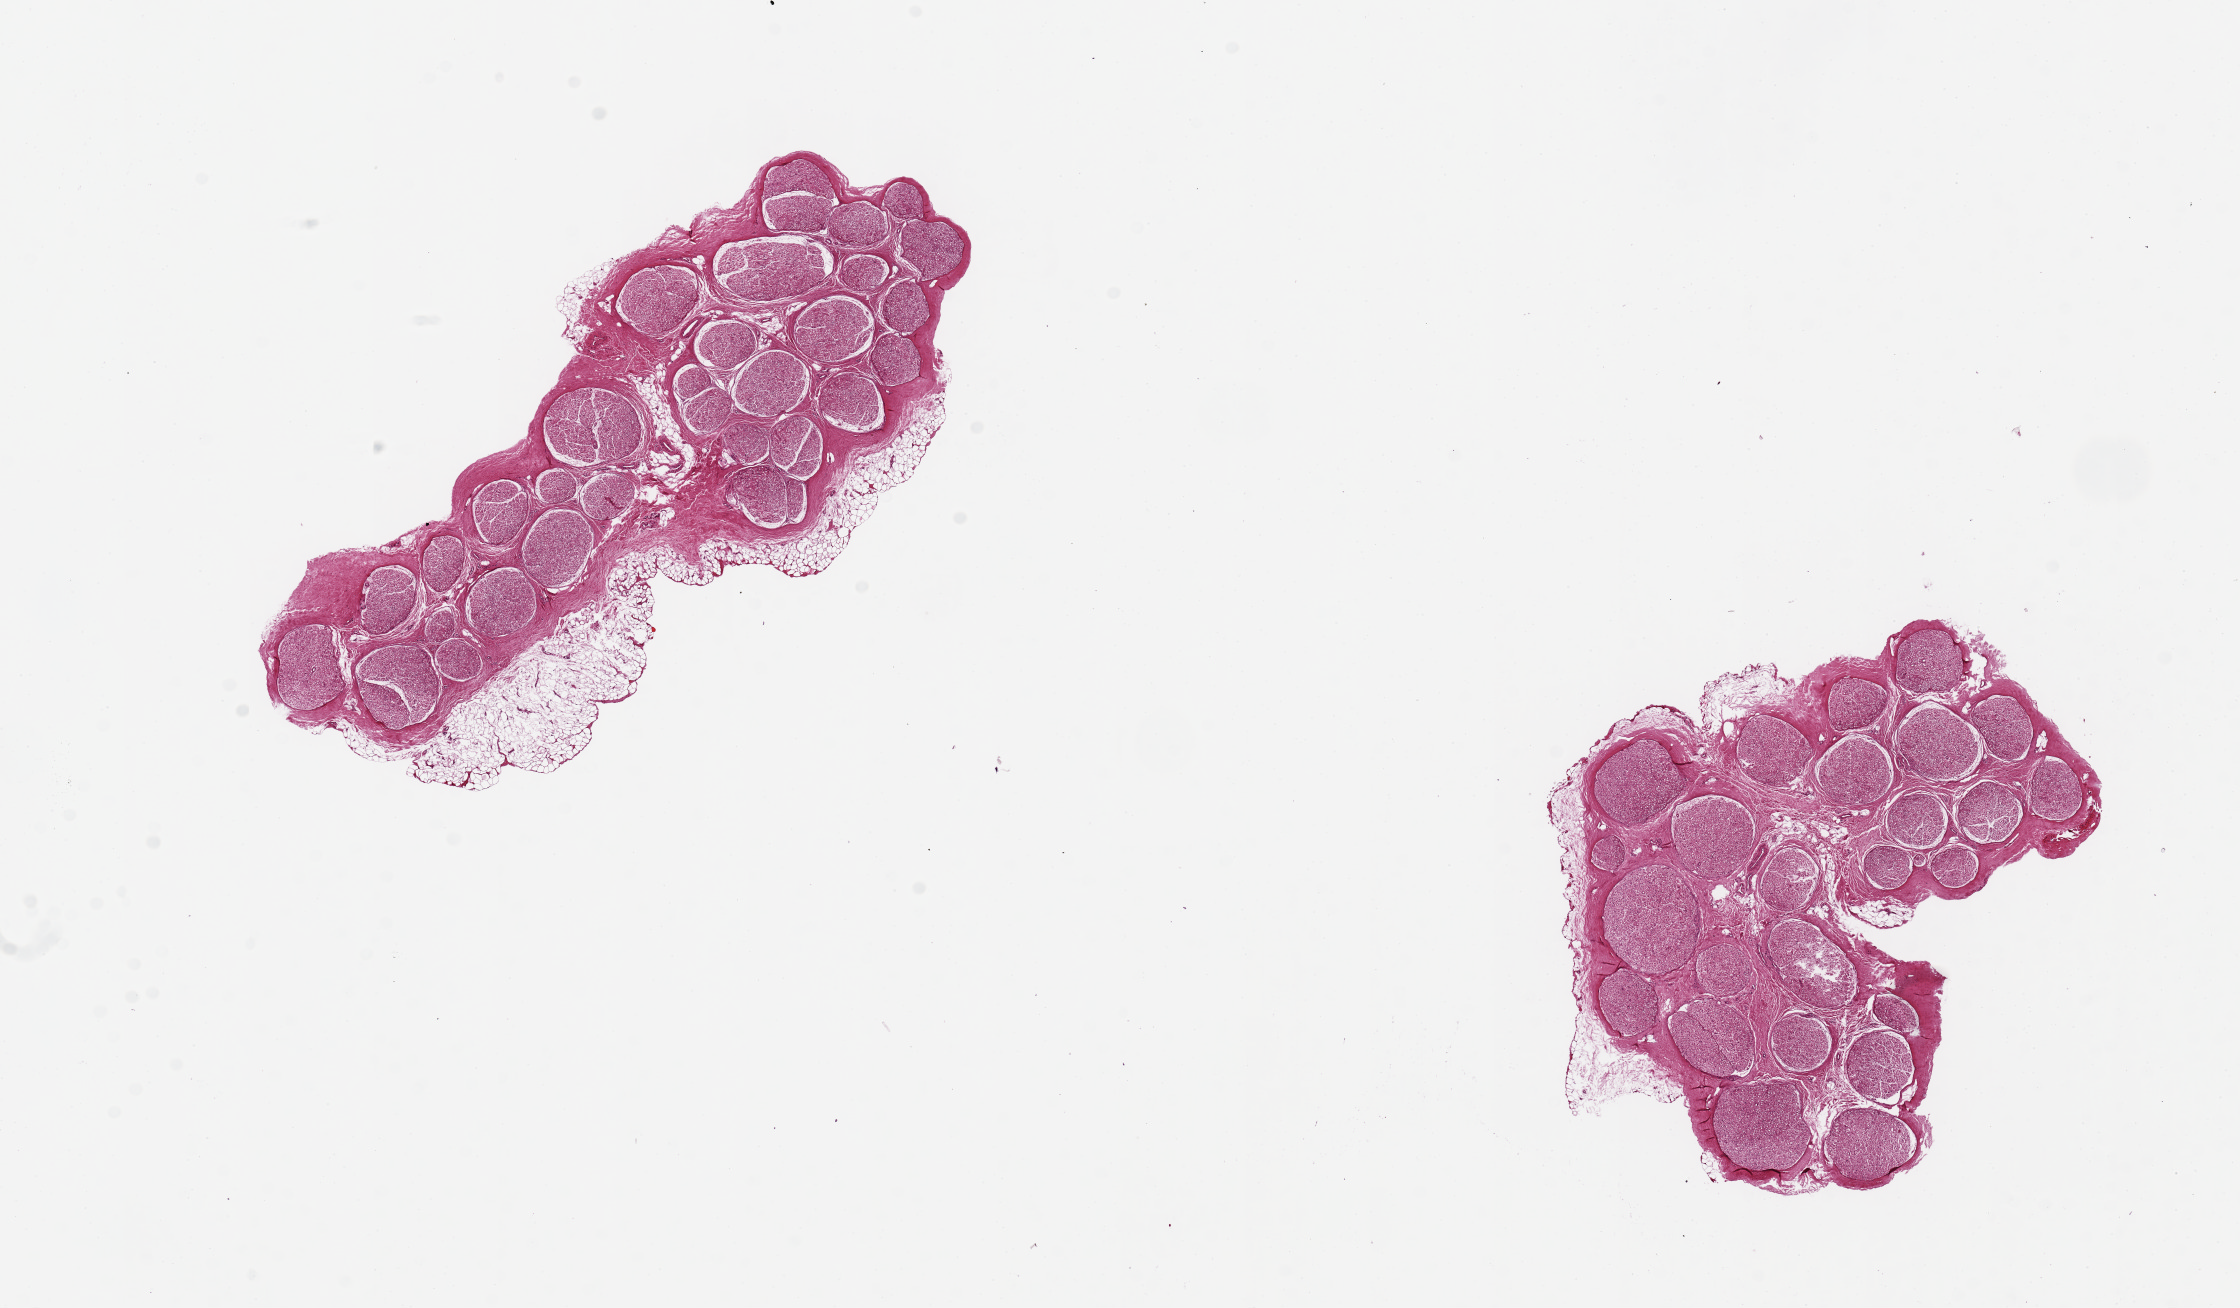
Digitized hematoxylin and eosin (H&E)-stained section, brightfield — a low-resolution overview of the entire scanned area, about 17.7 x 10.3 mm, PAXgene-fixed, paraffin-embedded tissue, sampled site (target tissue): tibial nerve, donor tissue sample.
- pathologist's review note for this sample: 2 pieces, ~ 5.5mm, partial rim of adherent fat on one, ~0.8mm